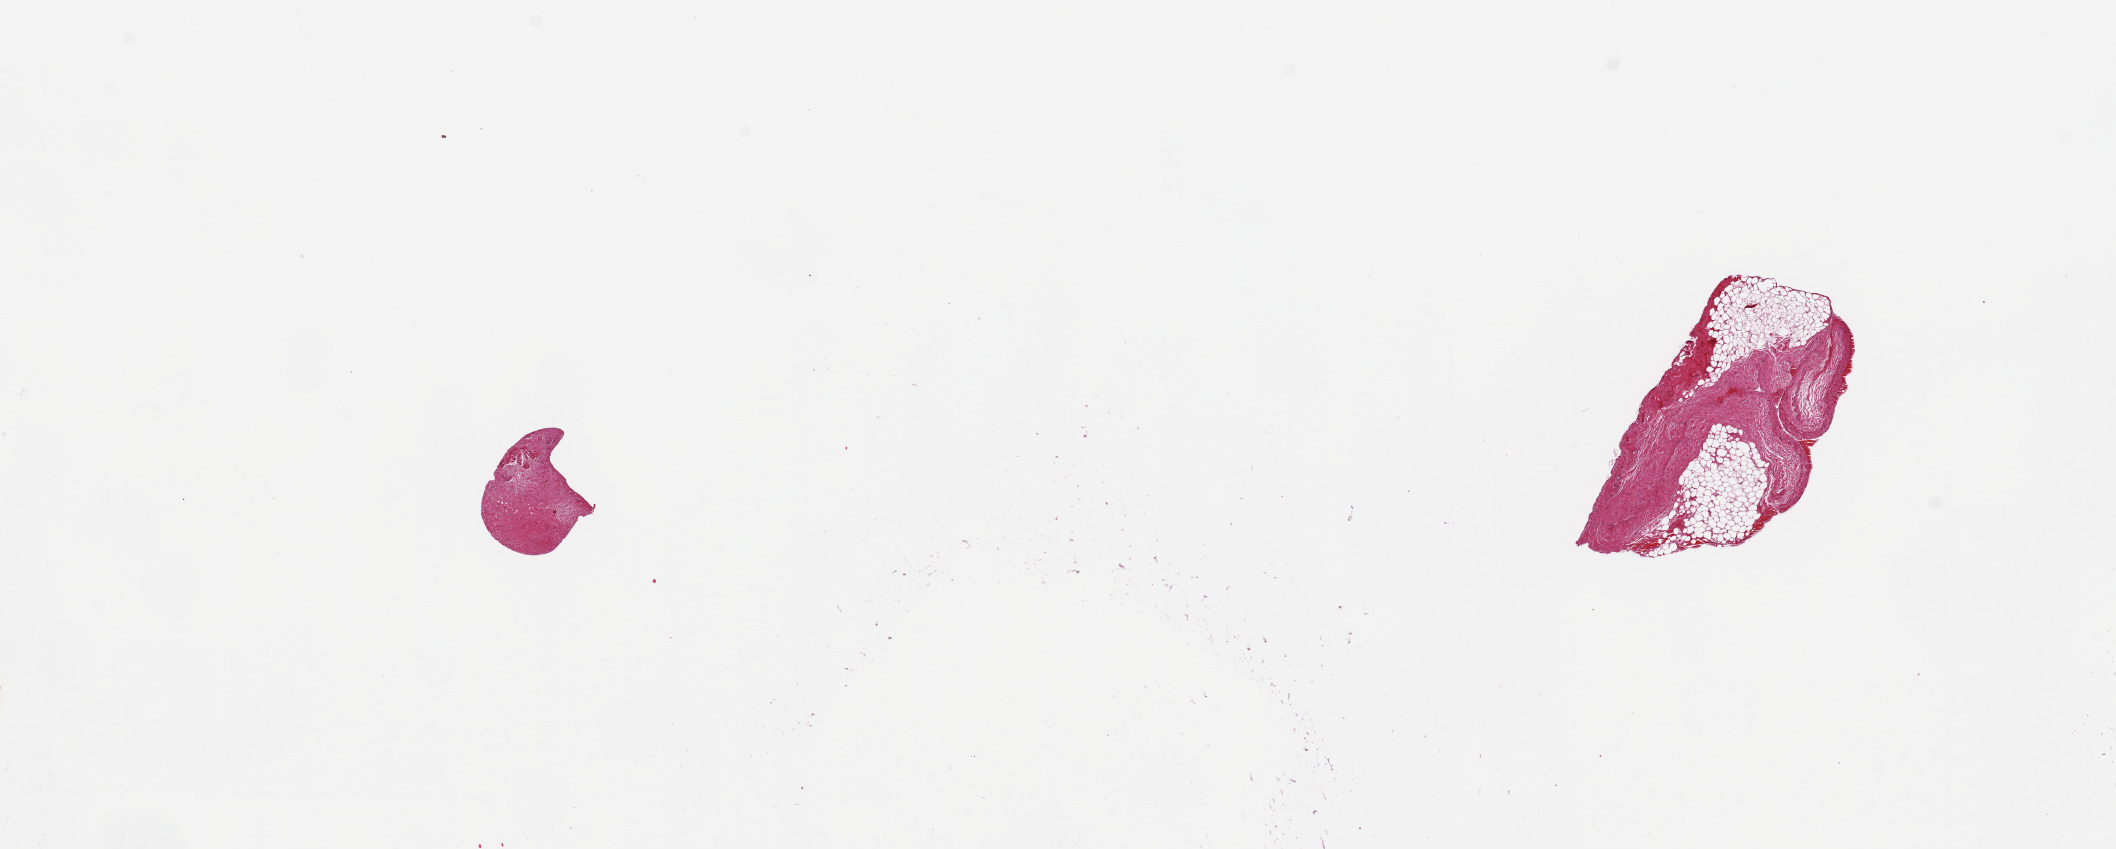
Haematoxylin and eosin whole-slide image, brightfield — low-resolution overview of the scanned area, about 16.7 x 6.7 mm, PAXgene-fixed, paraffin-embedded tissue, sampled site (target tissue): coronary artery, tissue donor sample. Male donor.
• reviewer comment on this tissue sample: 2 pieces, 2.5x1.5mm & 1mmx836um; no artery present, fibrofatty tissue, reject